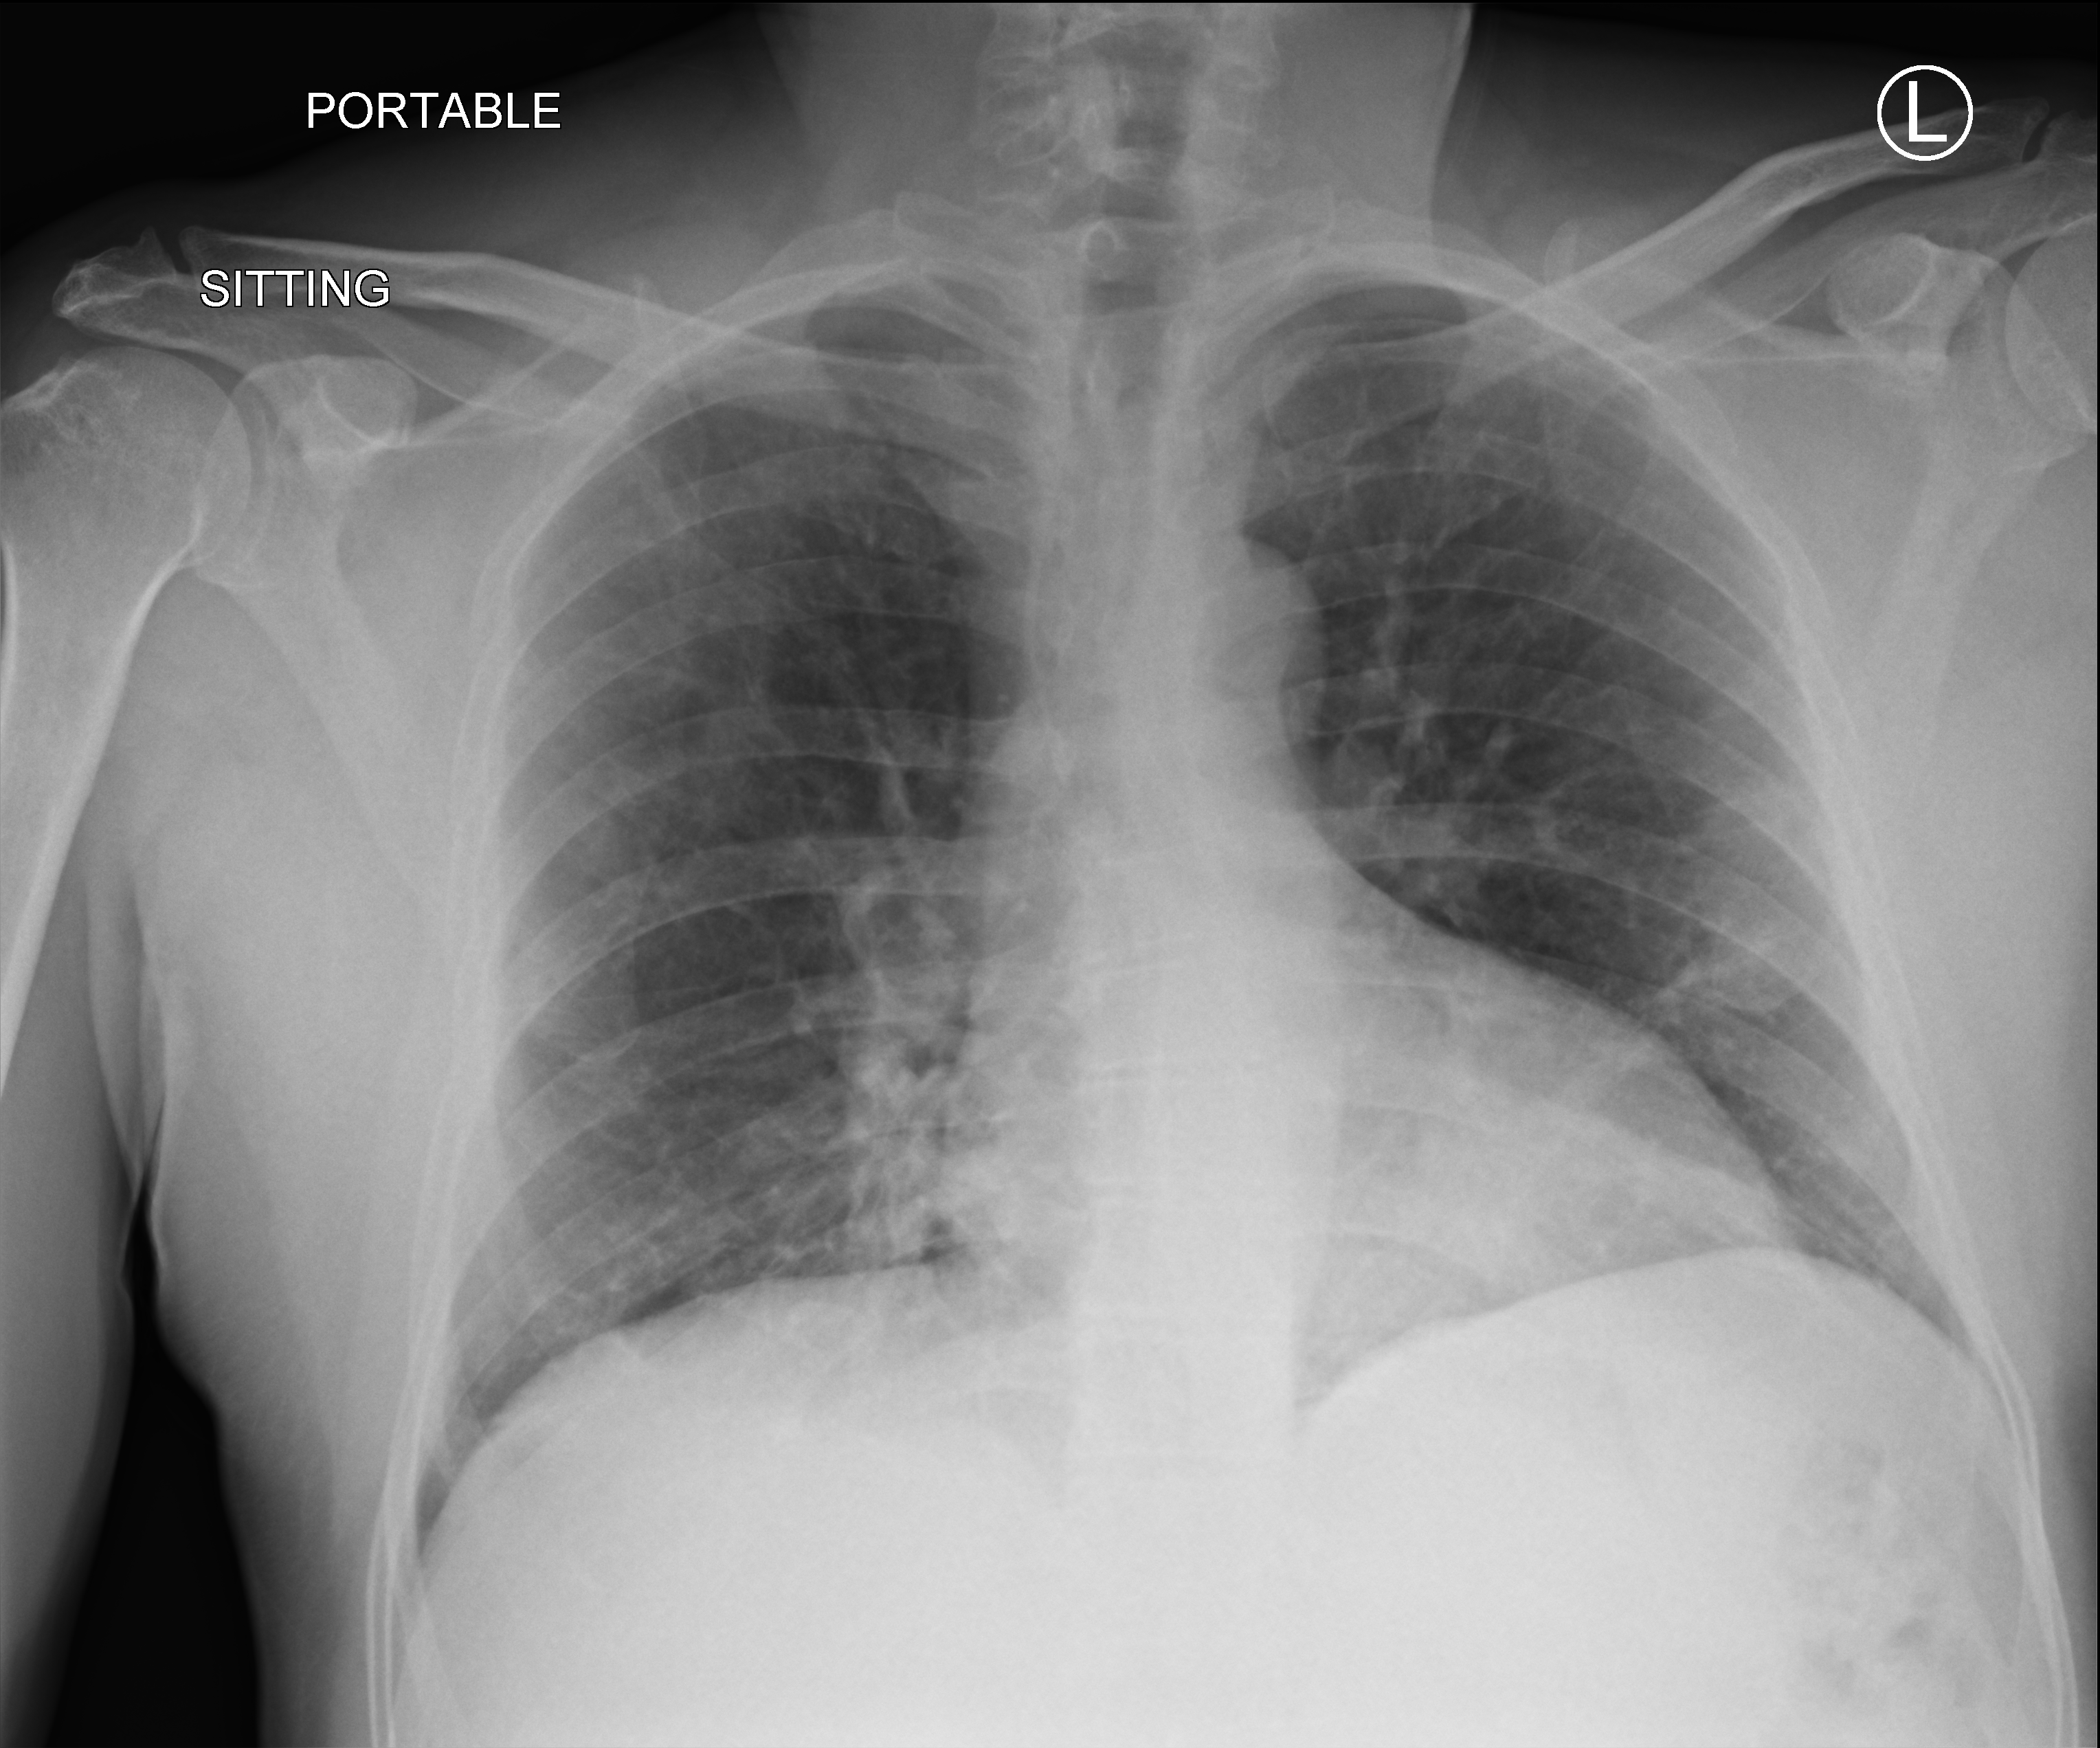
Bedside chest radiograph (computed radiography). Male patient hospitalised with COVID-19, age 18–59 years.
From the hospital-stay record, not from the radiograph (when in the stay this image was taken is not recorded):
- length of hospital stay: 1 day
- mechanically ventilated during this hospital stay: no
- chronic kidney disease (admission record): no